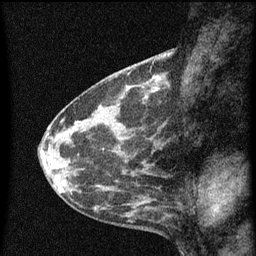
Breast MRI (dynamic contrast-enhanced), one sagittal slice. Position 24 of 60 along the scan axis. Dynamic contrast-enhanced series, image 2 of 3 at this slice position (ordered by acquisition). 1.5 T. TE 4.2 ms, TR 8 ms. 2 mm slice thickness. 256 × 256 image matrix, field of view 180 × 180 mm. Patient: female, 41 years.
Annotated regions visible in this slice (semi-automatically segmented with operator editing):
- analysis volume of interest (the breast-tissue region the enhancement analysis was run in; not a lesion): box from (x=130, y=76) to (x=157, y=103) px
- tumour enhancement mask (voxels above the 70 % enhancement threshold inside the analysis volume of interest): (x=136, y=76)–(x=157, y=101)